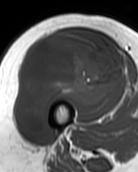
MRI of an extremity soft-tissue mass, one axial slice; slice 57 of 99 in the series (ordered by position); MR volume resampled by the dataset authors to the PET/CT grid (not the native acquisition matrix); 138 × 172 image matrix, field of view 135 × 168 mm. Female patient. Case-level facts recorded for this patient, not image findings: histological type: pleiomorphic undifferentiated sarcoma; grade: high; site of the primary tumour: right quadricep.
Annotated regions visible in this slice (expert contour drawn on MRI and transferred to this co-registered scan by the dataset authors):
- gross tumour volume including surrounding oedema: box from (x=16, y=32) to (x=122, y=135) px
- gross tumour volume (mass): (x=16, y=32)–(x=122, y=135)